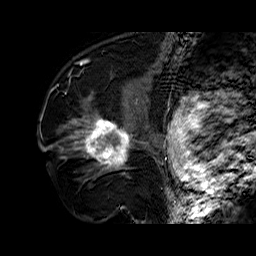
Breast MRI (dynamic contrast-enhanced), one sagittal slice. Slice 39 of 60 in the series (ordered by position). Dynamic contrast-enhanced series, time point 2 of 6 at this slice position (early post-contrast). 1.5 T. TE 6.4 ms, TR 32.7 ms. 4 mm slice thickness. 256 × 256 image matrix, field of view 200 × 200 mm. Female patient. Case-level facts recorded for this patient, not image findings: setting: breast cancer imaged before/during neoadjuvant chemotherapy; receptor status: HR-positive, HER2-negative.
Annotated regions visible in this slice (semi-automatically segmented with operator editing):
- analysis volume of interest (the breast-tissue region the enhancement analysis was run in; not a lesion): bounding box (x1, y1, x2, y2) in pixels: (73, 110, 141, 179)
- tumour enhancement mask (voxels above the 100 % enhancement threshold inside the analysis volume of interest): (76, 118, 132, 167)